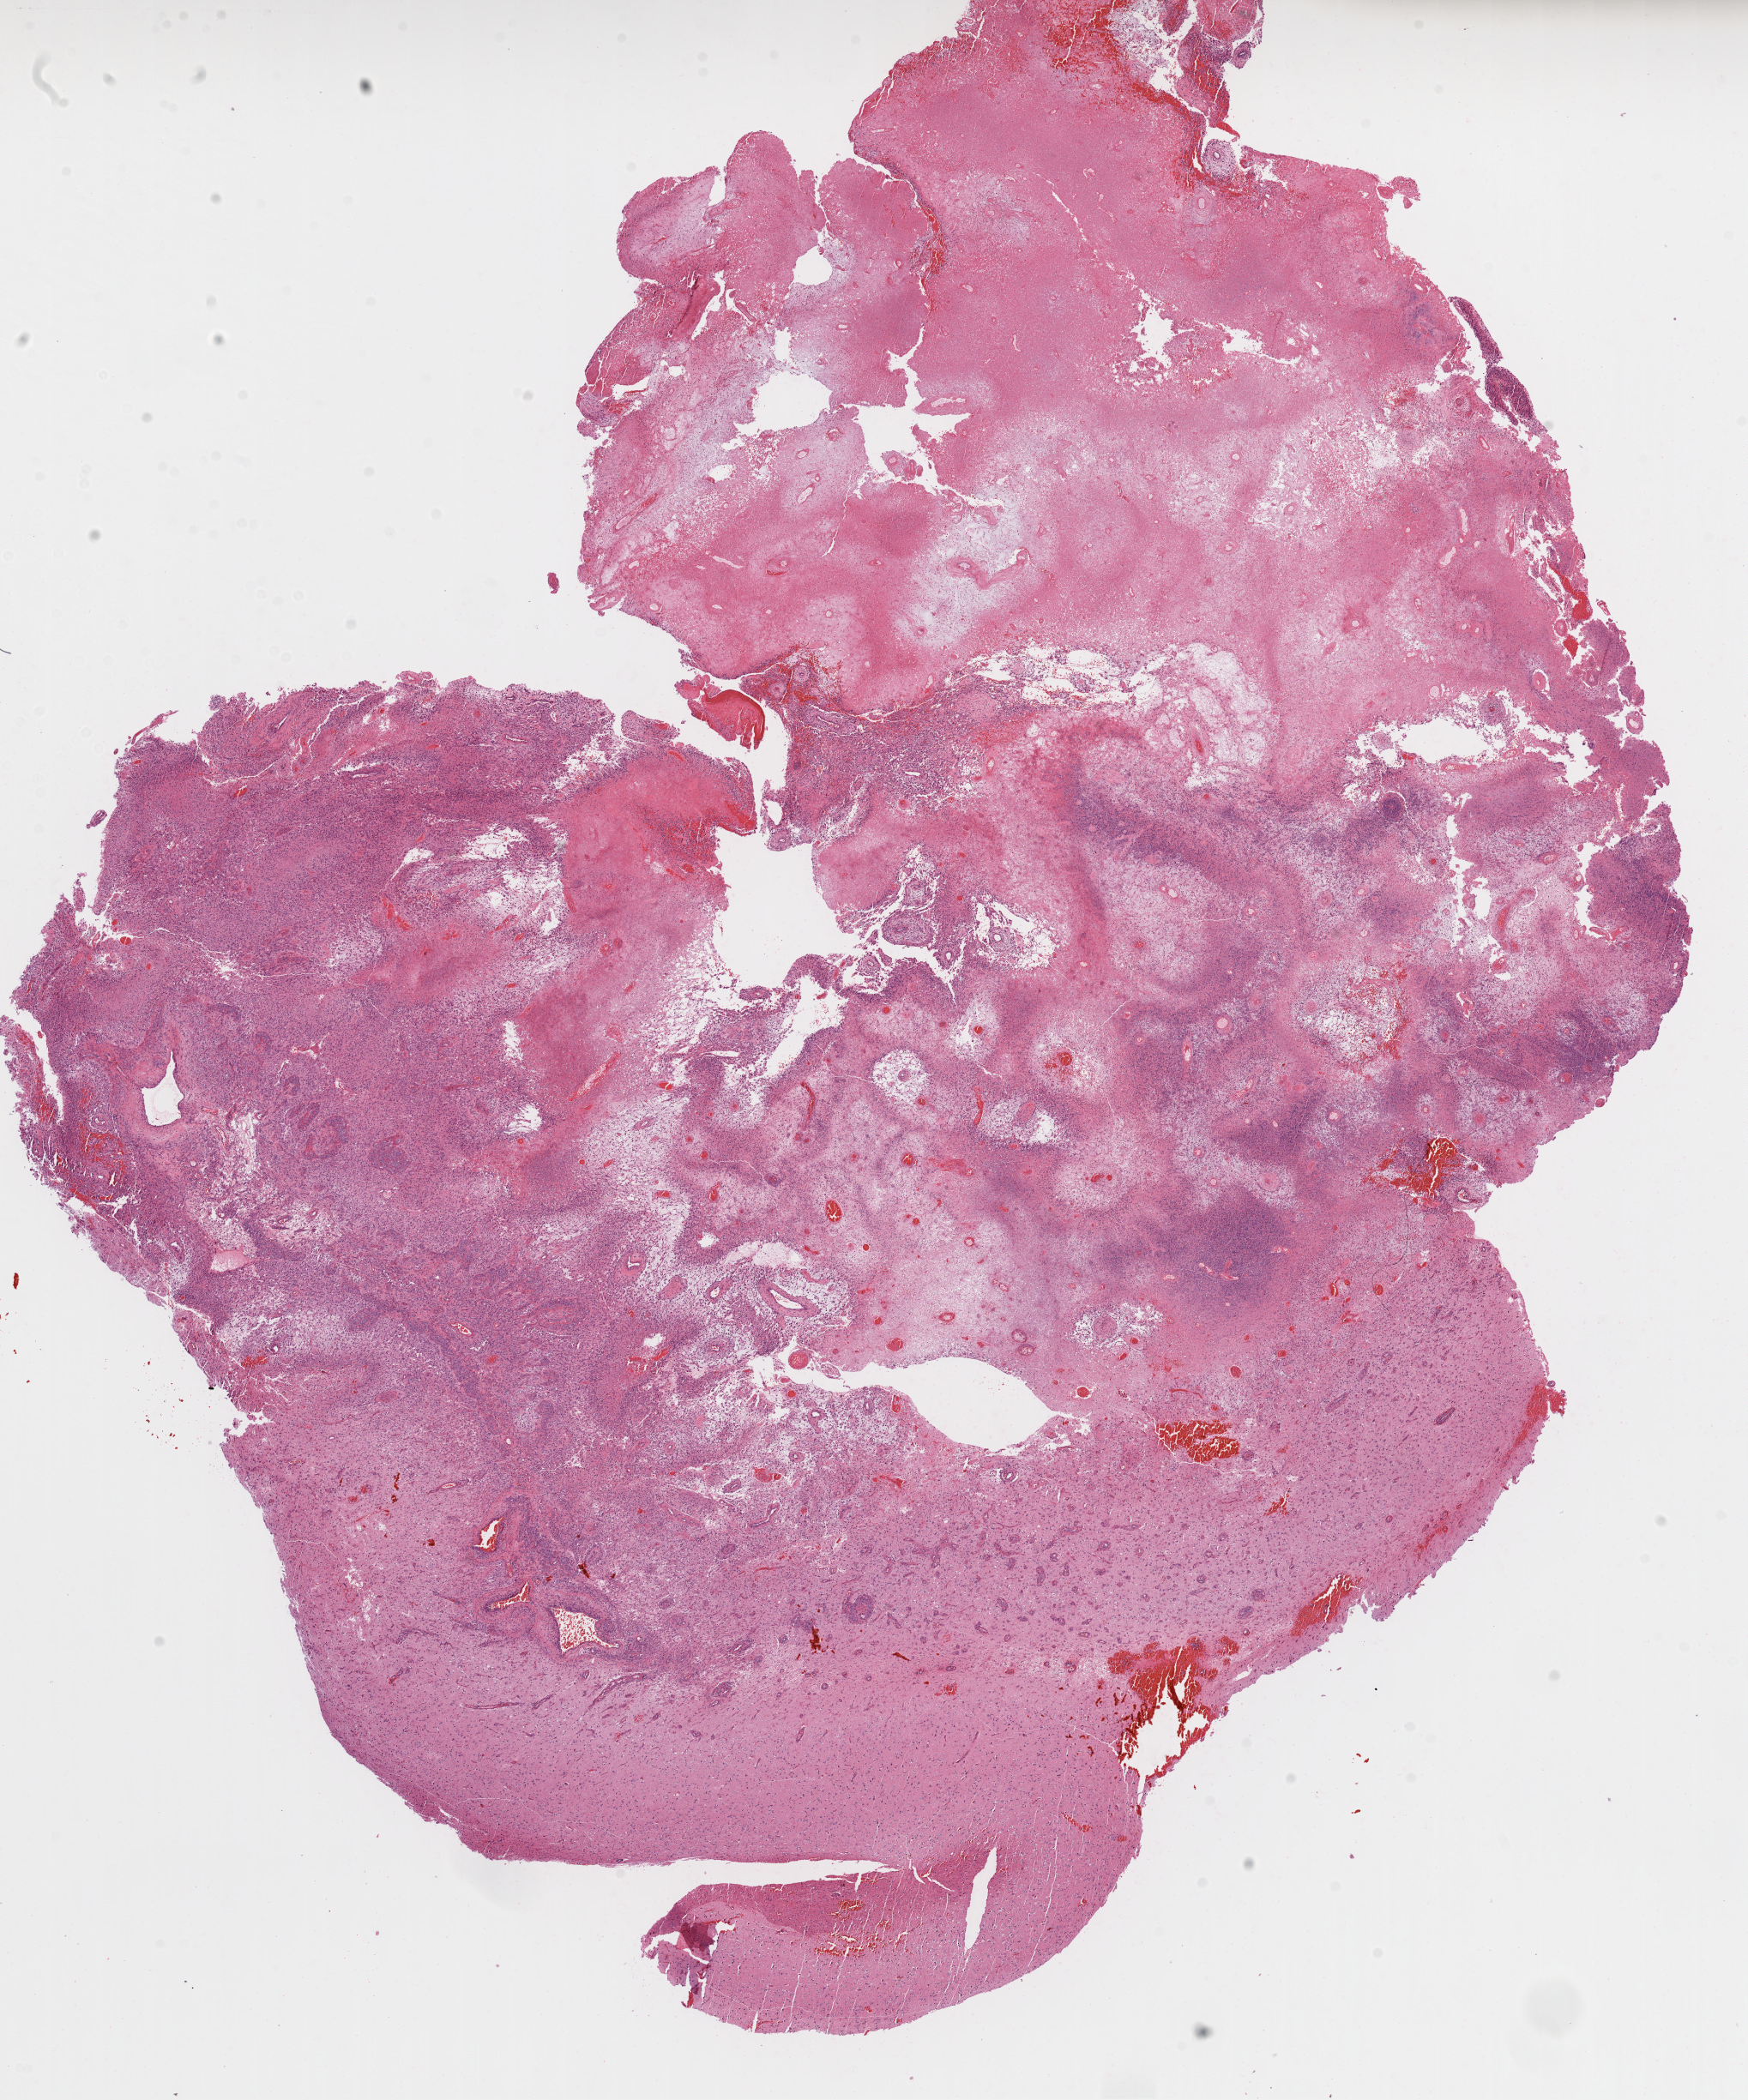
H&E-stained whole-slide image — shown as a low-resolution overview of the whole scanned area (about 16.4 x 19.8 mm, acquisition: 20x scan), formalin-fixed paraffin-embedded (FFPE) diagnostic section, sample: primary tumour, brain. Male patient; age at initial diagnosis 67 years.
Histologic diagnosis: Glioblastoma.